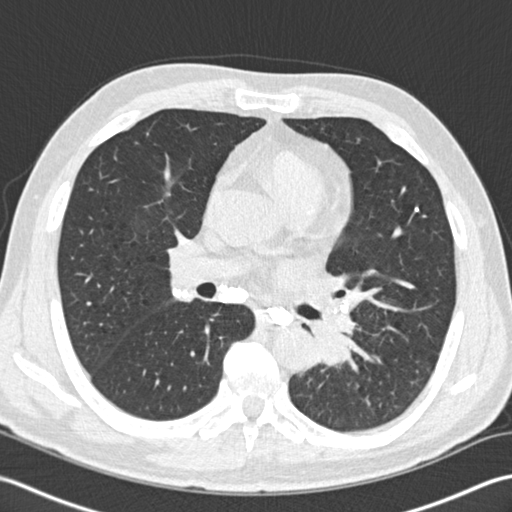
Low-dose screening chest CT, one axial slice; slice 96 of 170 in the series (ordered by position); 120 kVp; lung window (W 1500 / L -600 HU); 2 mm slice thickness; 512 × 512 image matrix, field of view 350 × 350 mm.
Structures marked on this image (manually delineated by an expert):
- lesion 1 (tumor, lower lobe of left lung): bounding box <316,320,357,367> (left, top, right, bottom; pixels)